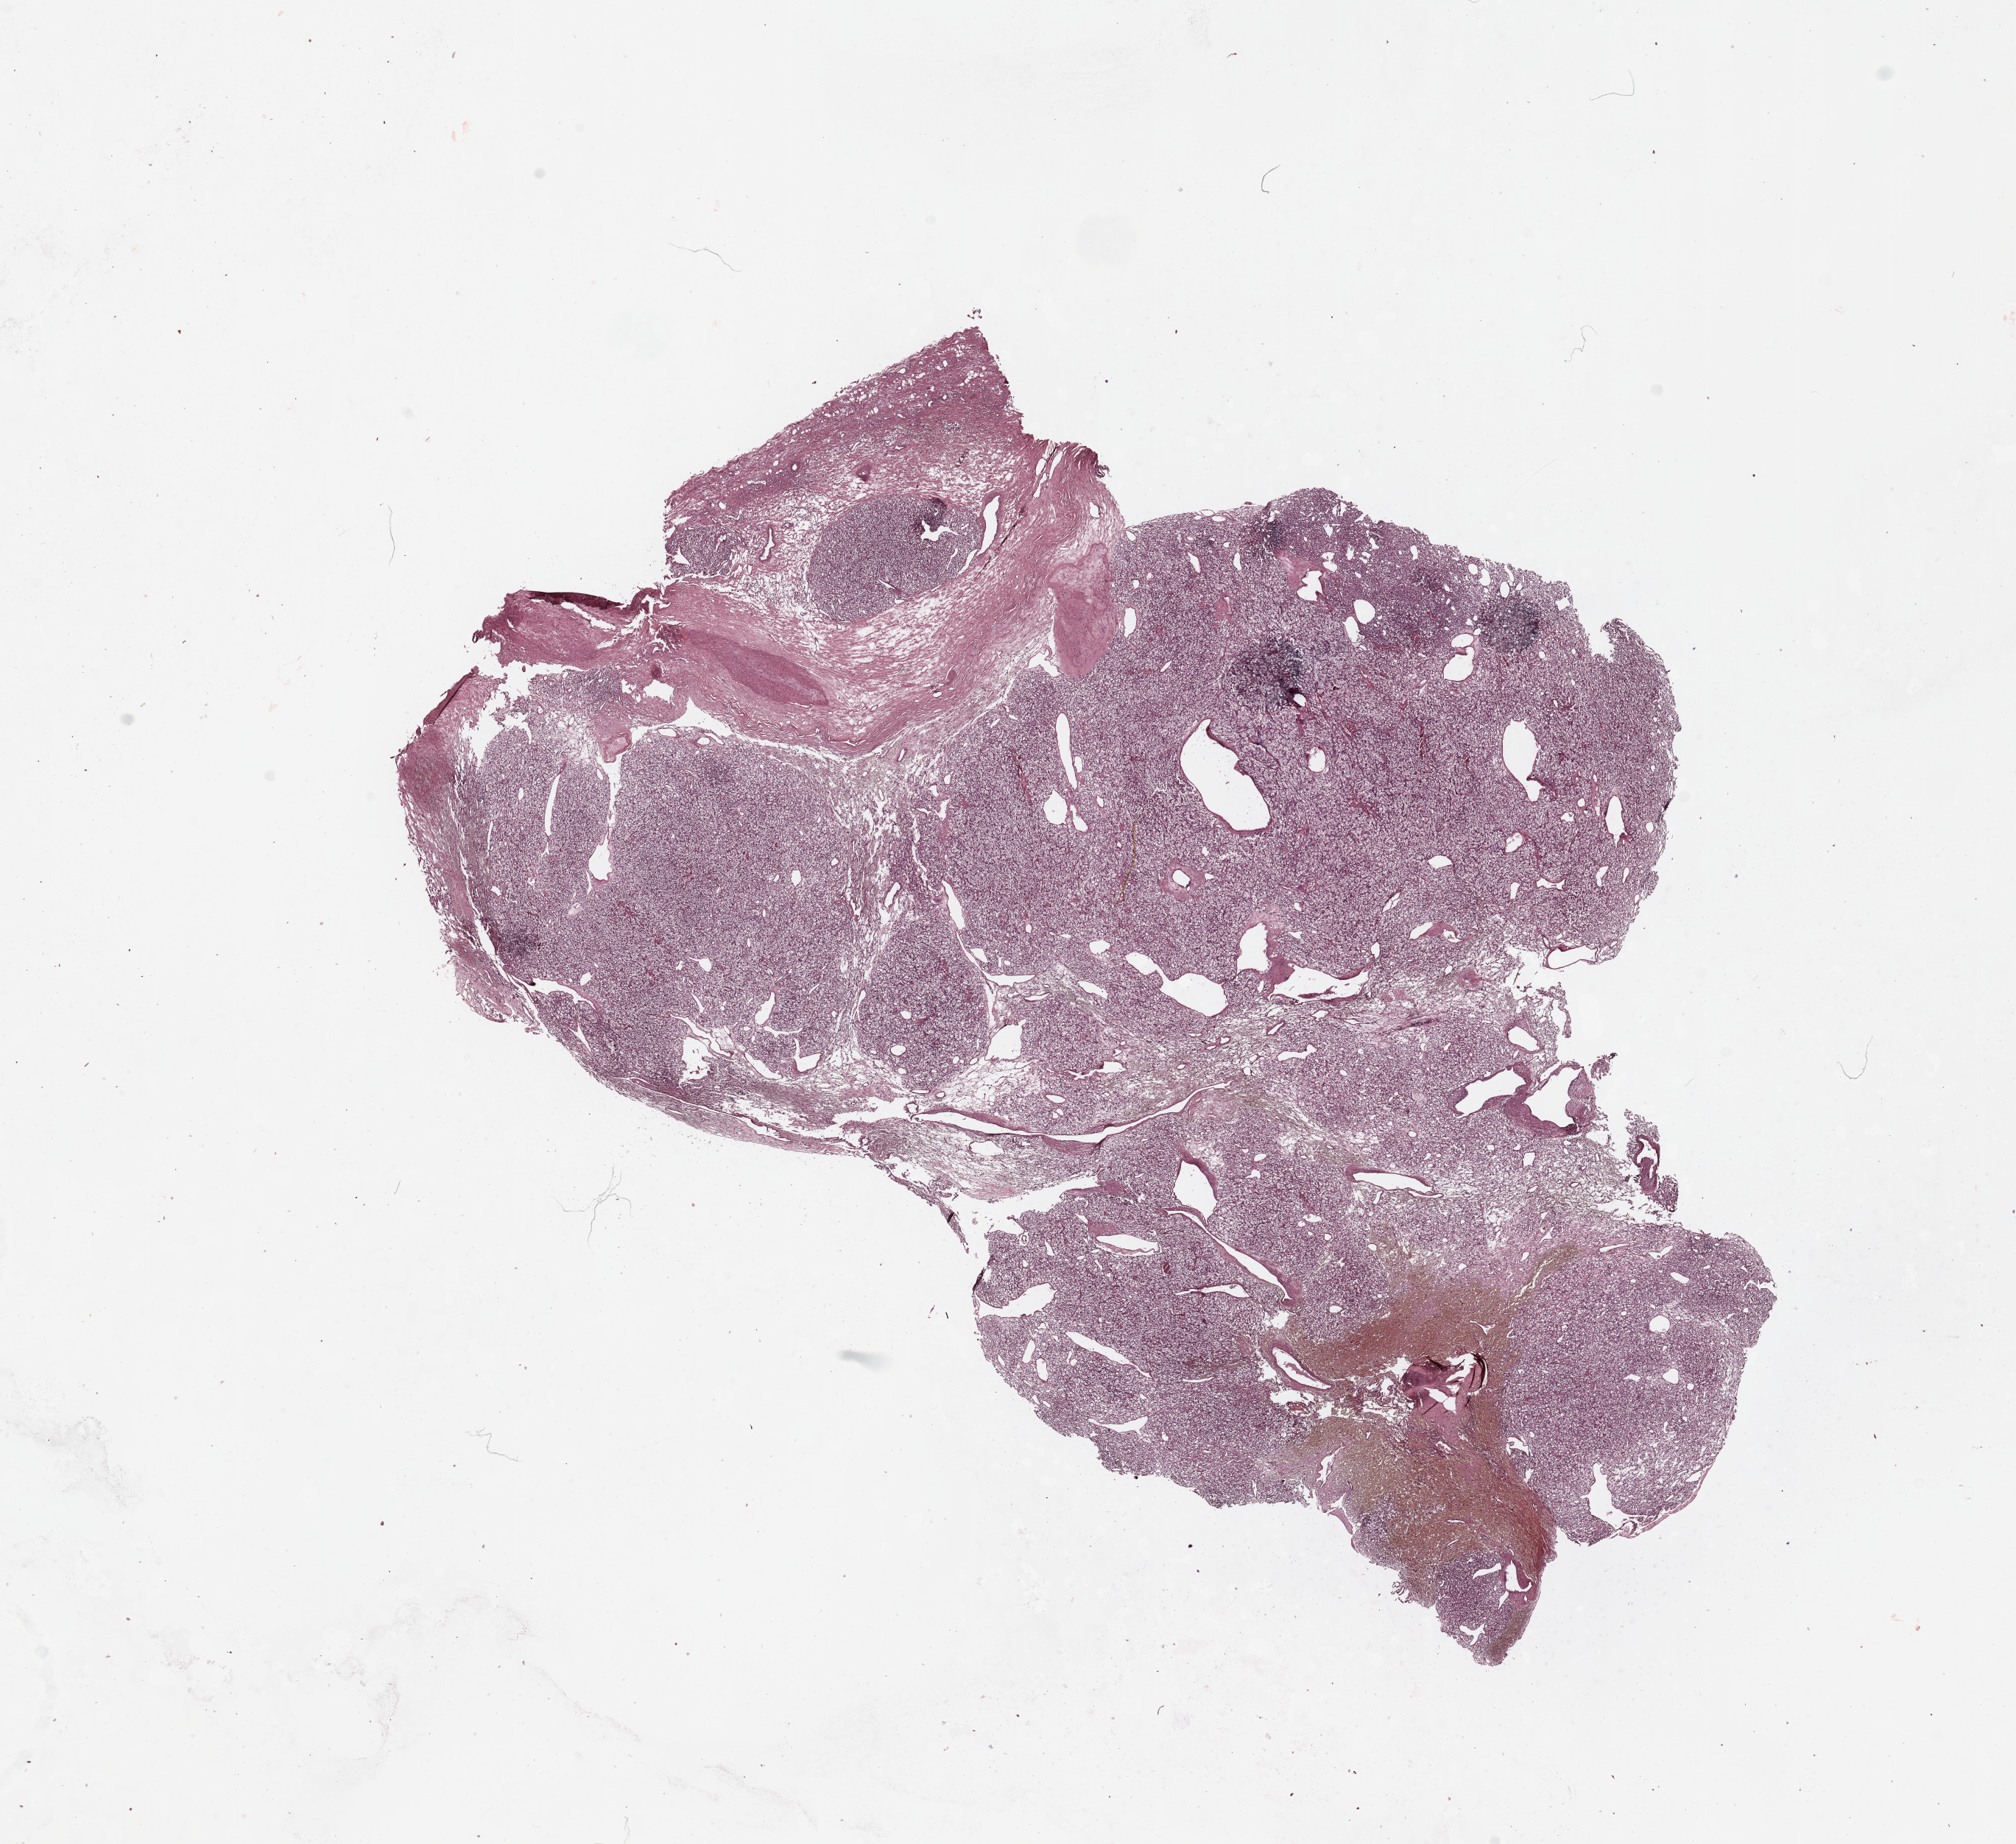
Whole-slide histology image, Hematoxylin and eosin (H&E) stained, a low-resolution overview of the entire scanned area, about 21.7 x 19.8 mm (slide scanned at 20x). Tumour tissue sample, sampled site: kidney. Patient: male, age 67 years. Histologic grade: G1 (well differentiated). Composition of this section per pathologist review: tumour nuclei 90%, necrosis 10%.
Primary tumour site (as recorded): upper pole. AJCC pathologic stage: I. Histologic diagnosis: Renal cell carcinoma, NOS.